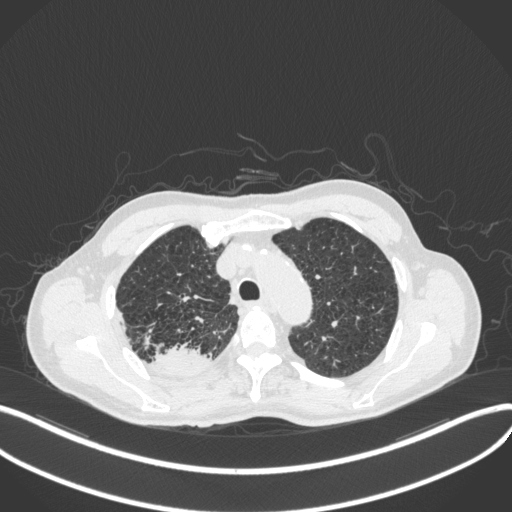
Chest CT, one axial slice; slice 343 of 423 in the series (ordered by position); 120 kVp; lung window (W 1500 / L -600 HU); 512 × 512 image matrix, field of view 400 × 400 mm. Male patient, age 79 years. Case-level facts recorded for this patient, not image findings: clinical TNM (as recorded): T3 N0 M0.
Annotated regions visible in this slice (bounding box drawn by a radiologist):
- lung tumour (recorded histology: adenocarcinoma): box from (x=149, y=343) to (x=207, y=373) px